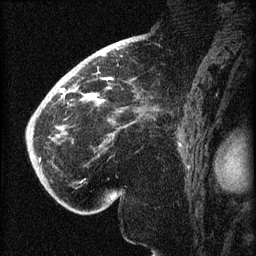
Breast MRI (dynamic contrast-enhanced), one sagittal slice; slice 46 of 60 in the series (ordered by position); dynamic contrast-enhanced series, image 2 of 3 at this slice position (ordered by acquisition); 1.5 T; TE 4.2 ms, TR 8.2 ms; 2 mm slice thickness; 256 × 256 image matrix. Female patient, age 71 years.
Annotated regions visible in this slice (semi-automatic segmentation, software-assisted and operator-edited):
- analysis volume of interest (the breast-tissue region the enhancement analysis was run in; not a lesion): box from (x=40, y=72) to (x=148, y=196) px
- tumour enhancement mask (voxels above the 70 % enhancement threshold inside the analysis volume of interest): (x=40, y=87)–(x=103, y=161)